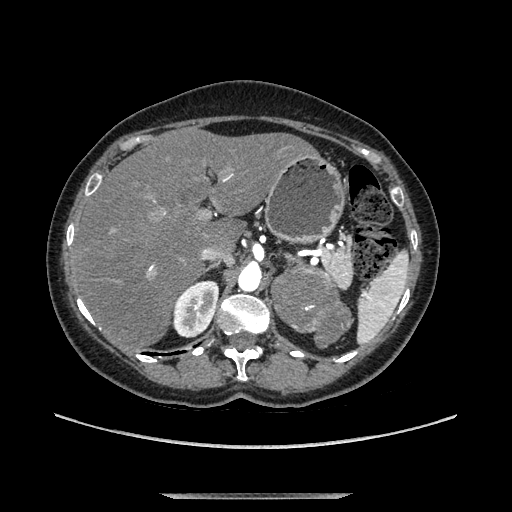
Contrast-enhanced abdominal CT, one axial slice; slice 85 of 169 in the series (ordered by position); soft-tissue window (W 400 / L 40 HU); 1.25 mm slice thickness; 512 × 512 image matrix, field of view 400 × 400 mm. Female patient. From the clinical record (not read from this slice): diagnosis: adrenocortical carcinoma; tumour side: left adrenal; tumour size at pathology: 9 cm; Ki-67 index: 2 %; stage (as recorded): 3.
Structures marked on this image (semi-automatically segmented with operator editing):
- mass: box from (x=276, y=255) to (x=350, y=346) px